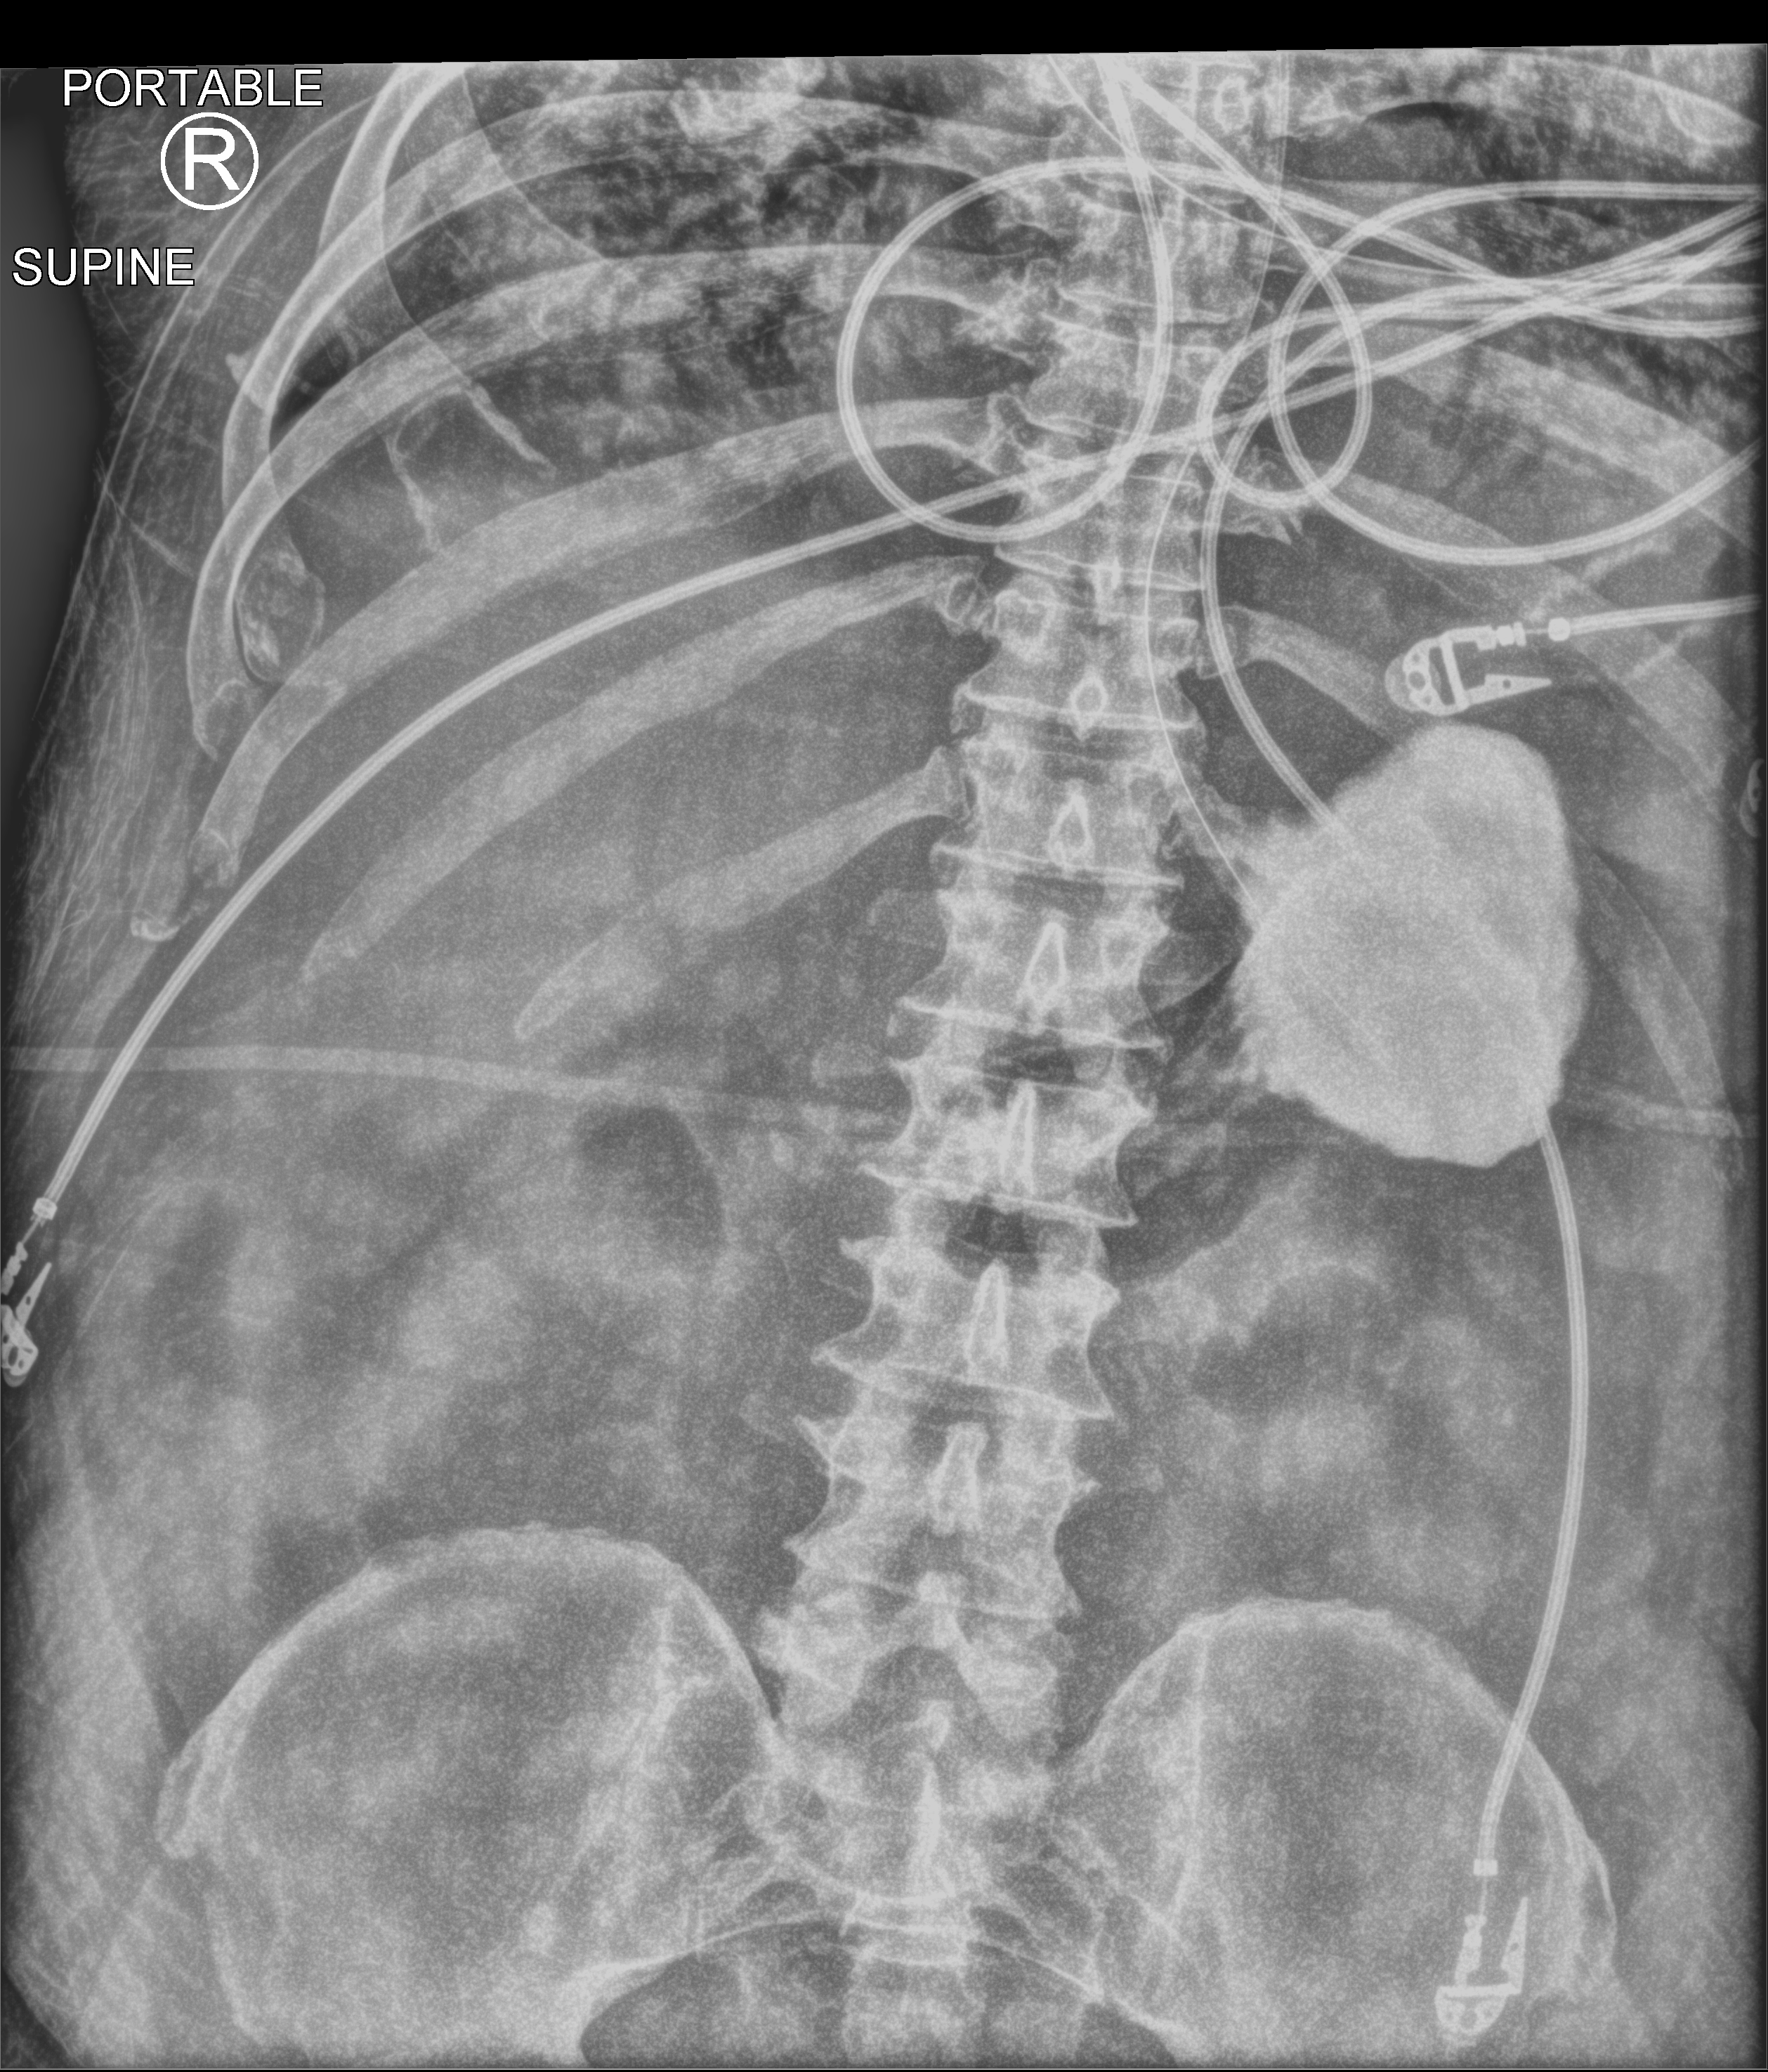
Portable abdomen radiograph, anteroposterior (AP) projection. Patient hospitalised with COVID-19; male, aged 60–74 years.
From the hospital-stay record, not from the radiograph (when in the stay this image was taken is not recorded):
- mechanically ventilated during this hospital stay: yes